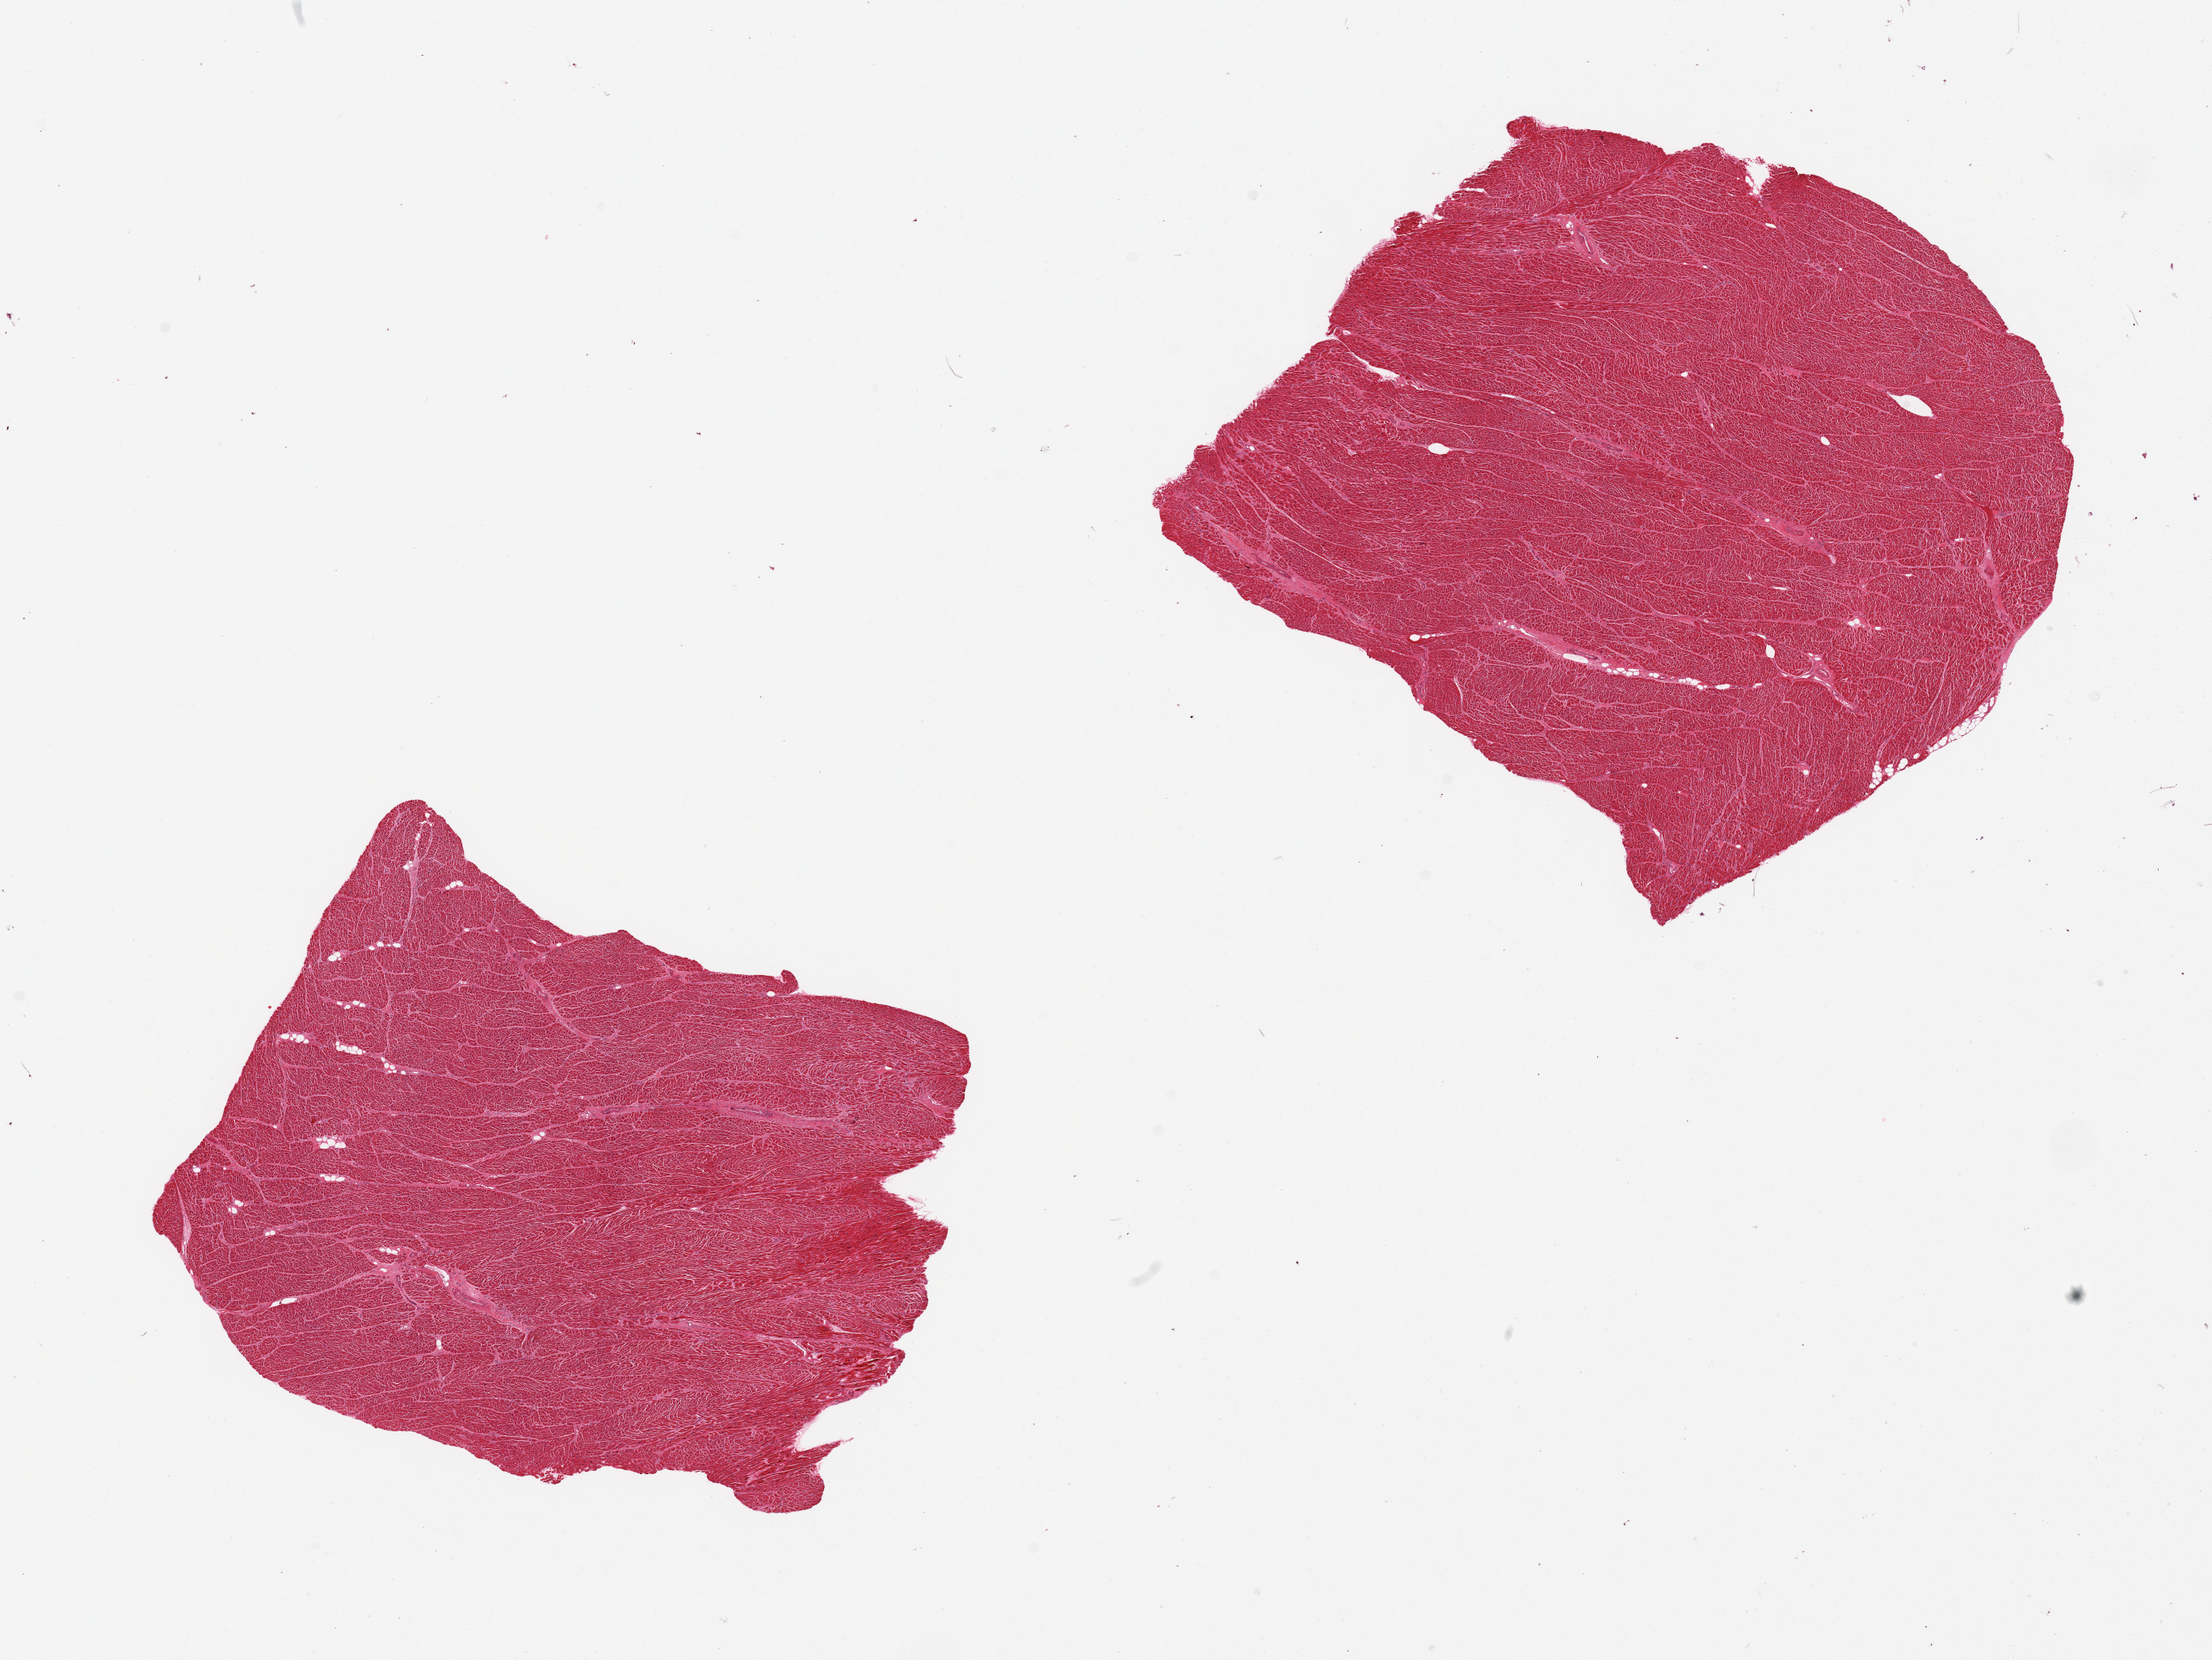
Whole-slide image, haematoxylin and eosin stain, a low-resolution overview of the entire scanned area, about 21.7 x 16.3 mm; PAXgene-fixed paraffin-embedded (PFPE) section; sampled site (target tissue): heart; donor tissue sample. Female donor.
Pathologist's review note for this sample: 2 pieces.